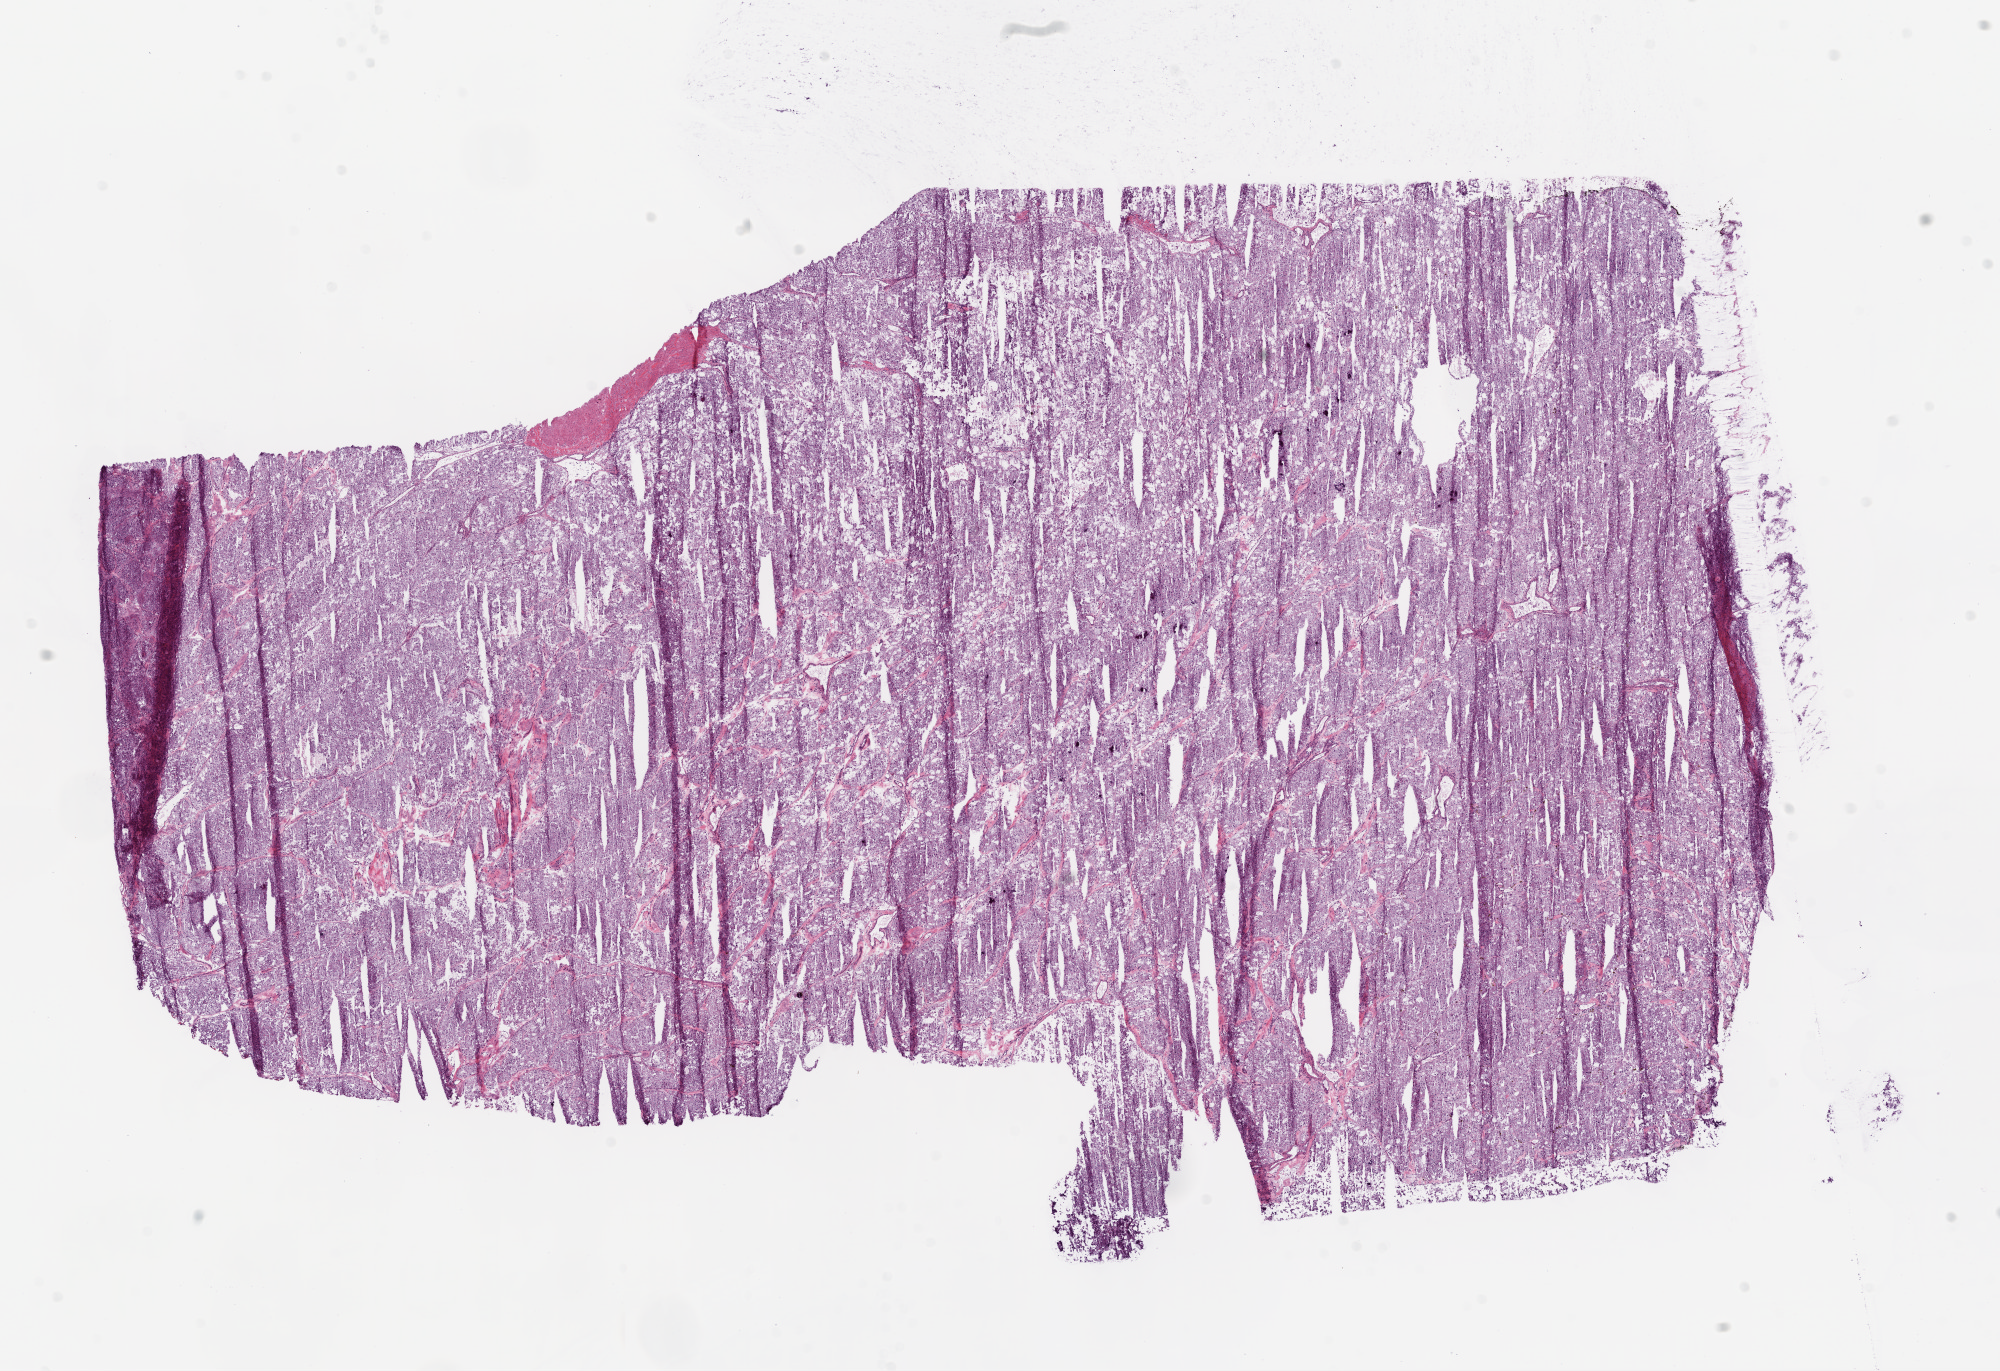
Digitized H&E-stained tissue section (whole slide), whole scanned area (about 16.0 x 11.0 mm, slide scanned at 20x) shown as a low-resolution overview; frozen section; sample: primary tumour, kidney. Male, age 59 years at initial diagnosis. Histologic grade: G2 (moderately differentiated). Pathologist review of this section (percent, as recorded): tumour cells 97%, tumour nuclei 90%, normal cells 0%, stromal cells 3%, necrosis 0%.
AJCC pathologic stage: II. Laterality: right. Histologic diagnosis: Clear cell adenocarcinoma, NOS. TNM: T2 NX M0.